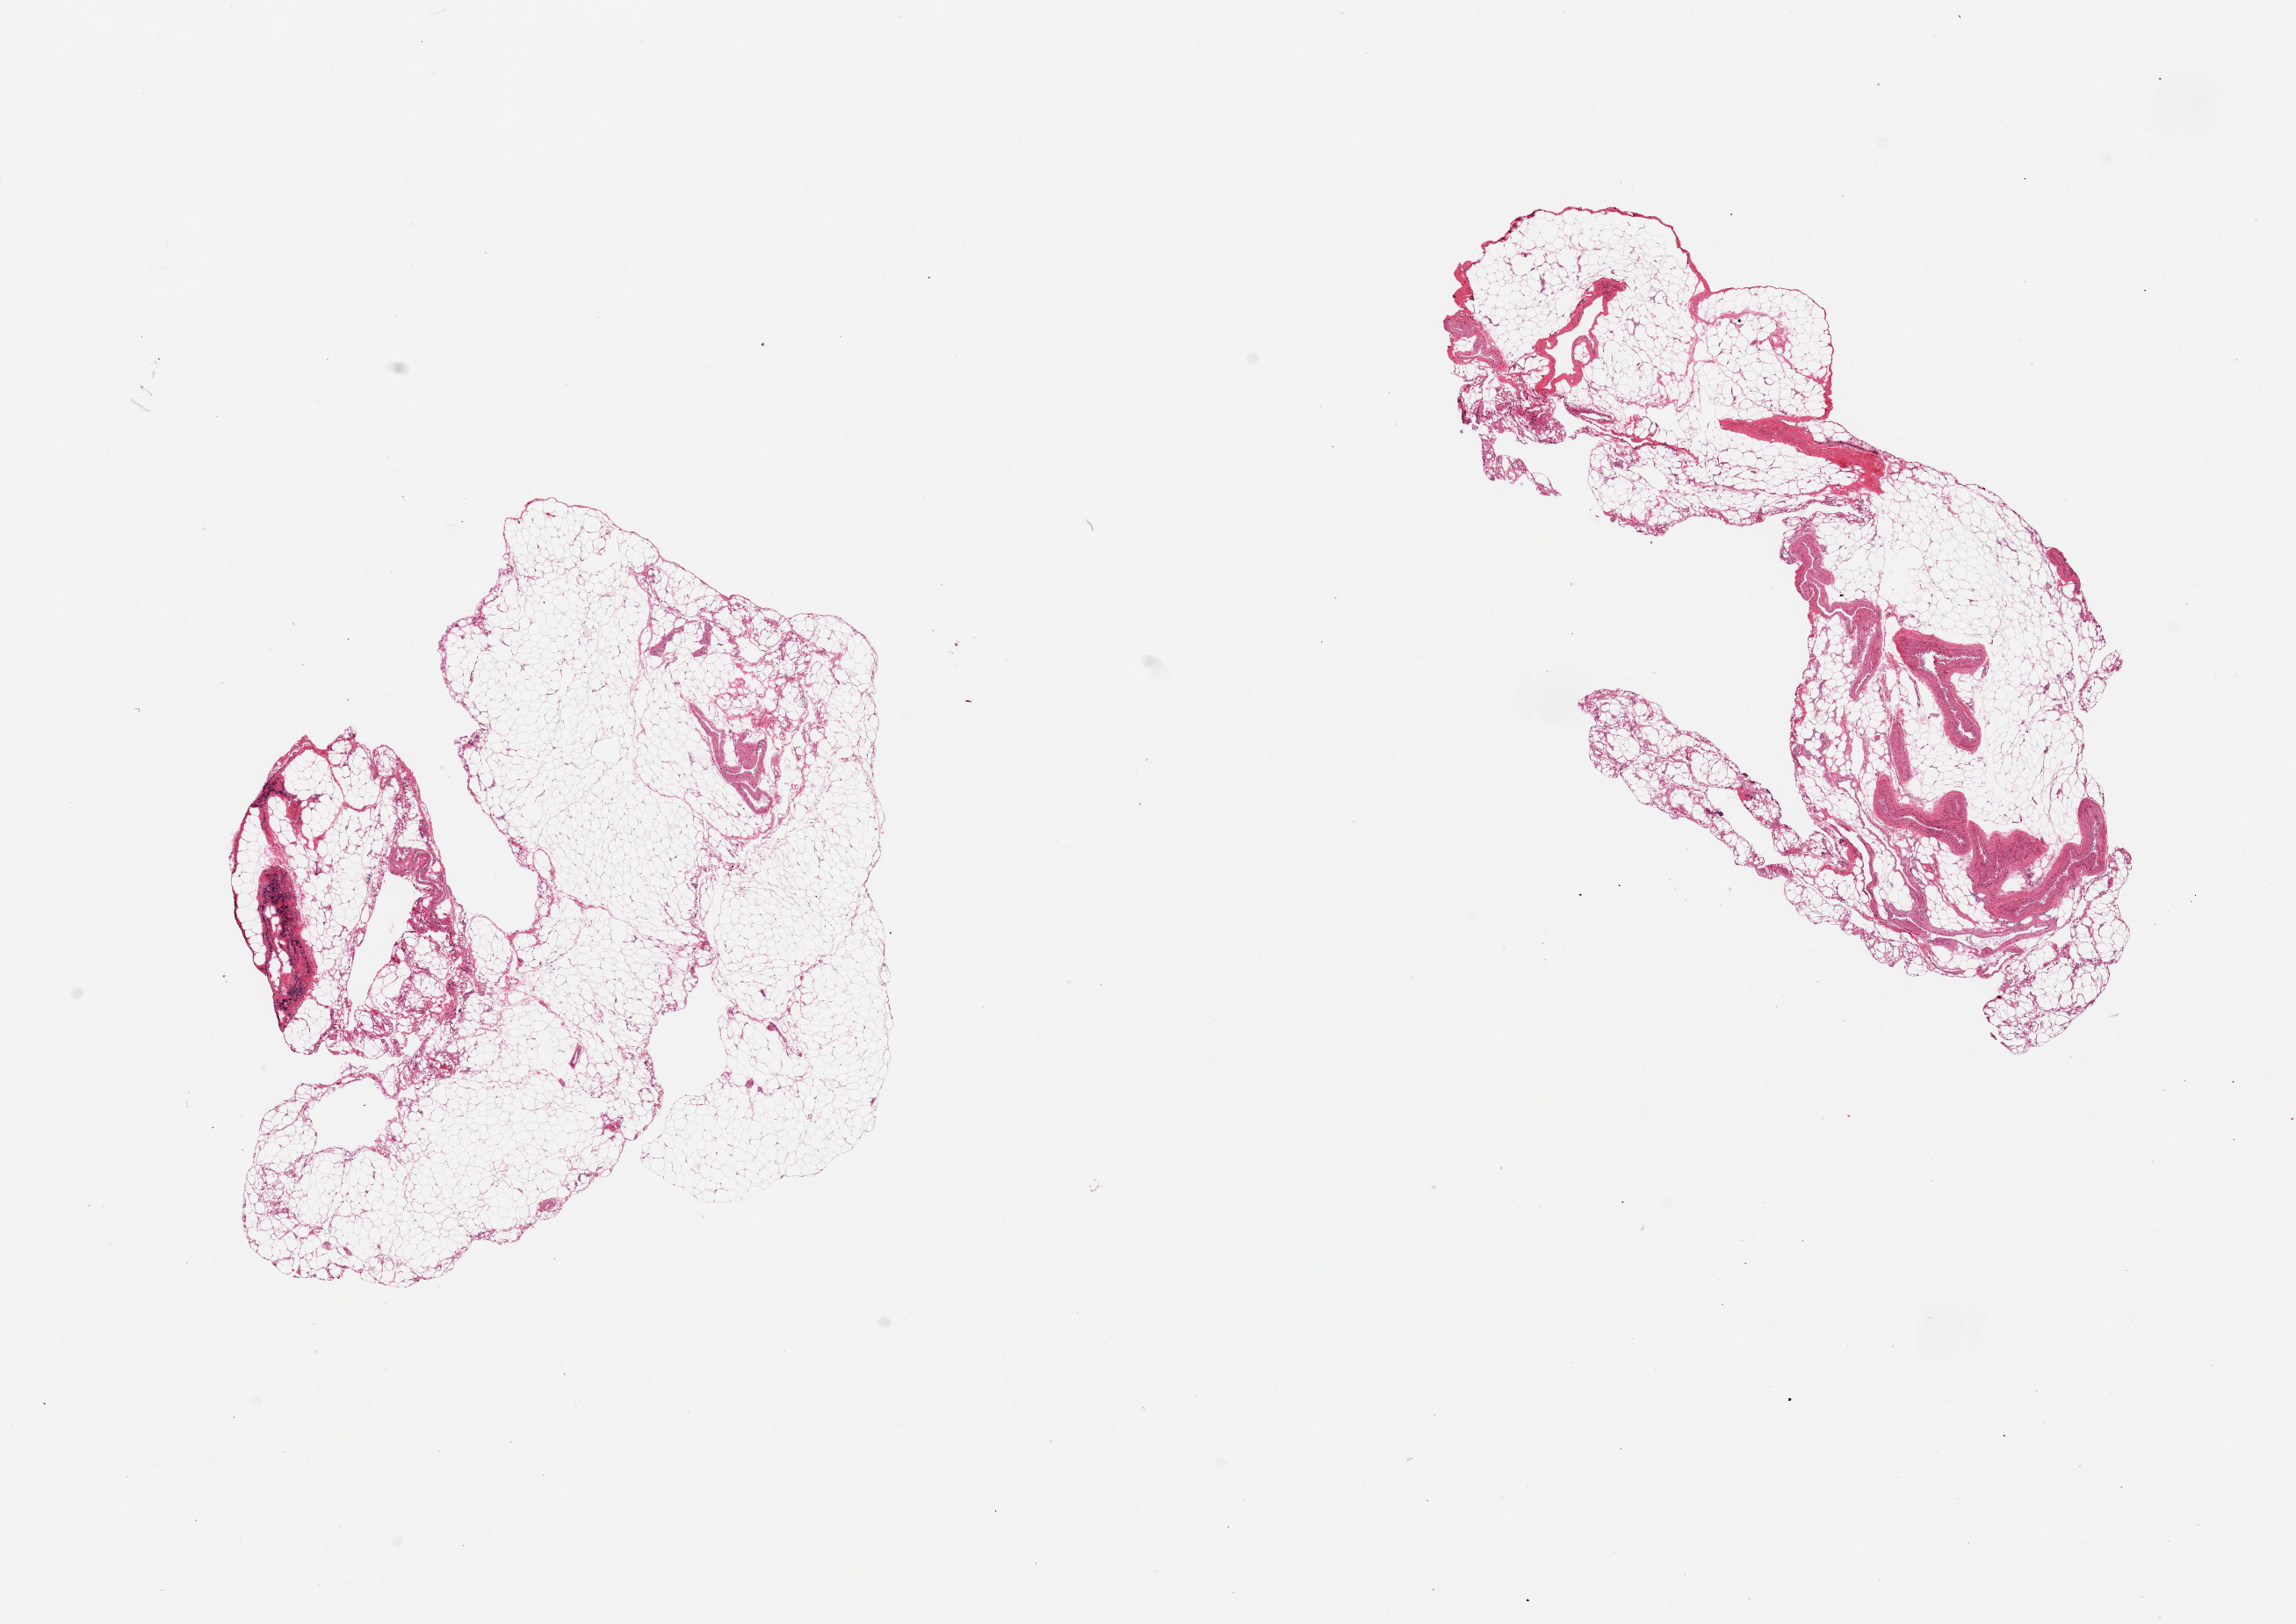
Digitized hematoxylin and eosin (H&E)-stained section, brightfield — whole scanned area (about 20.7 x 14.6 mm) shown as a low-resolution overview, PAXgene-fixed paraffin-embedded (PFPE) section, section of omentum (target tissue), tissue donor sample. Donor sex: male.
Pathologist's review note for this sample: 2 pieces, 20% fibrovascular tissue.